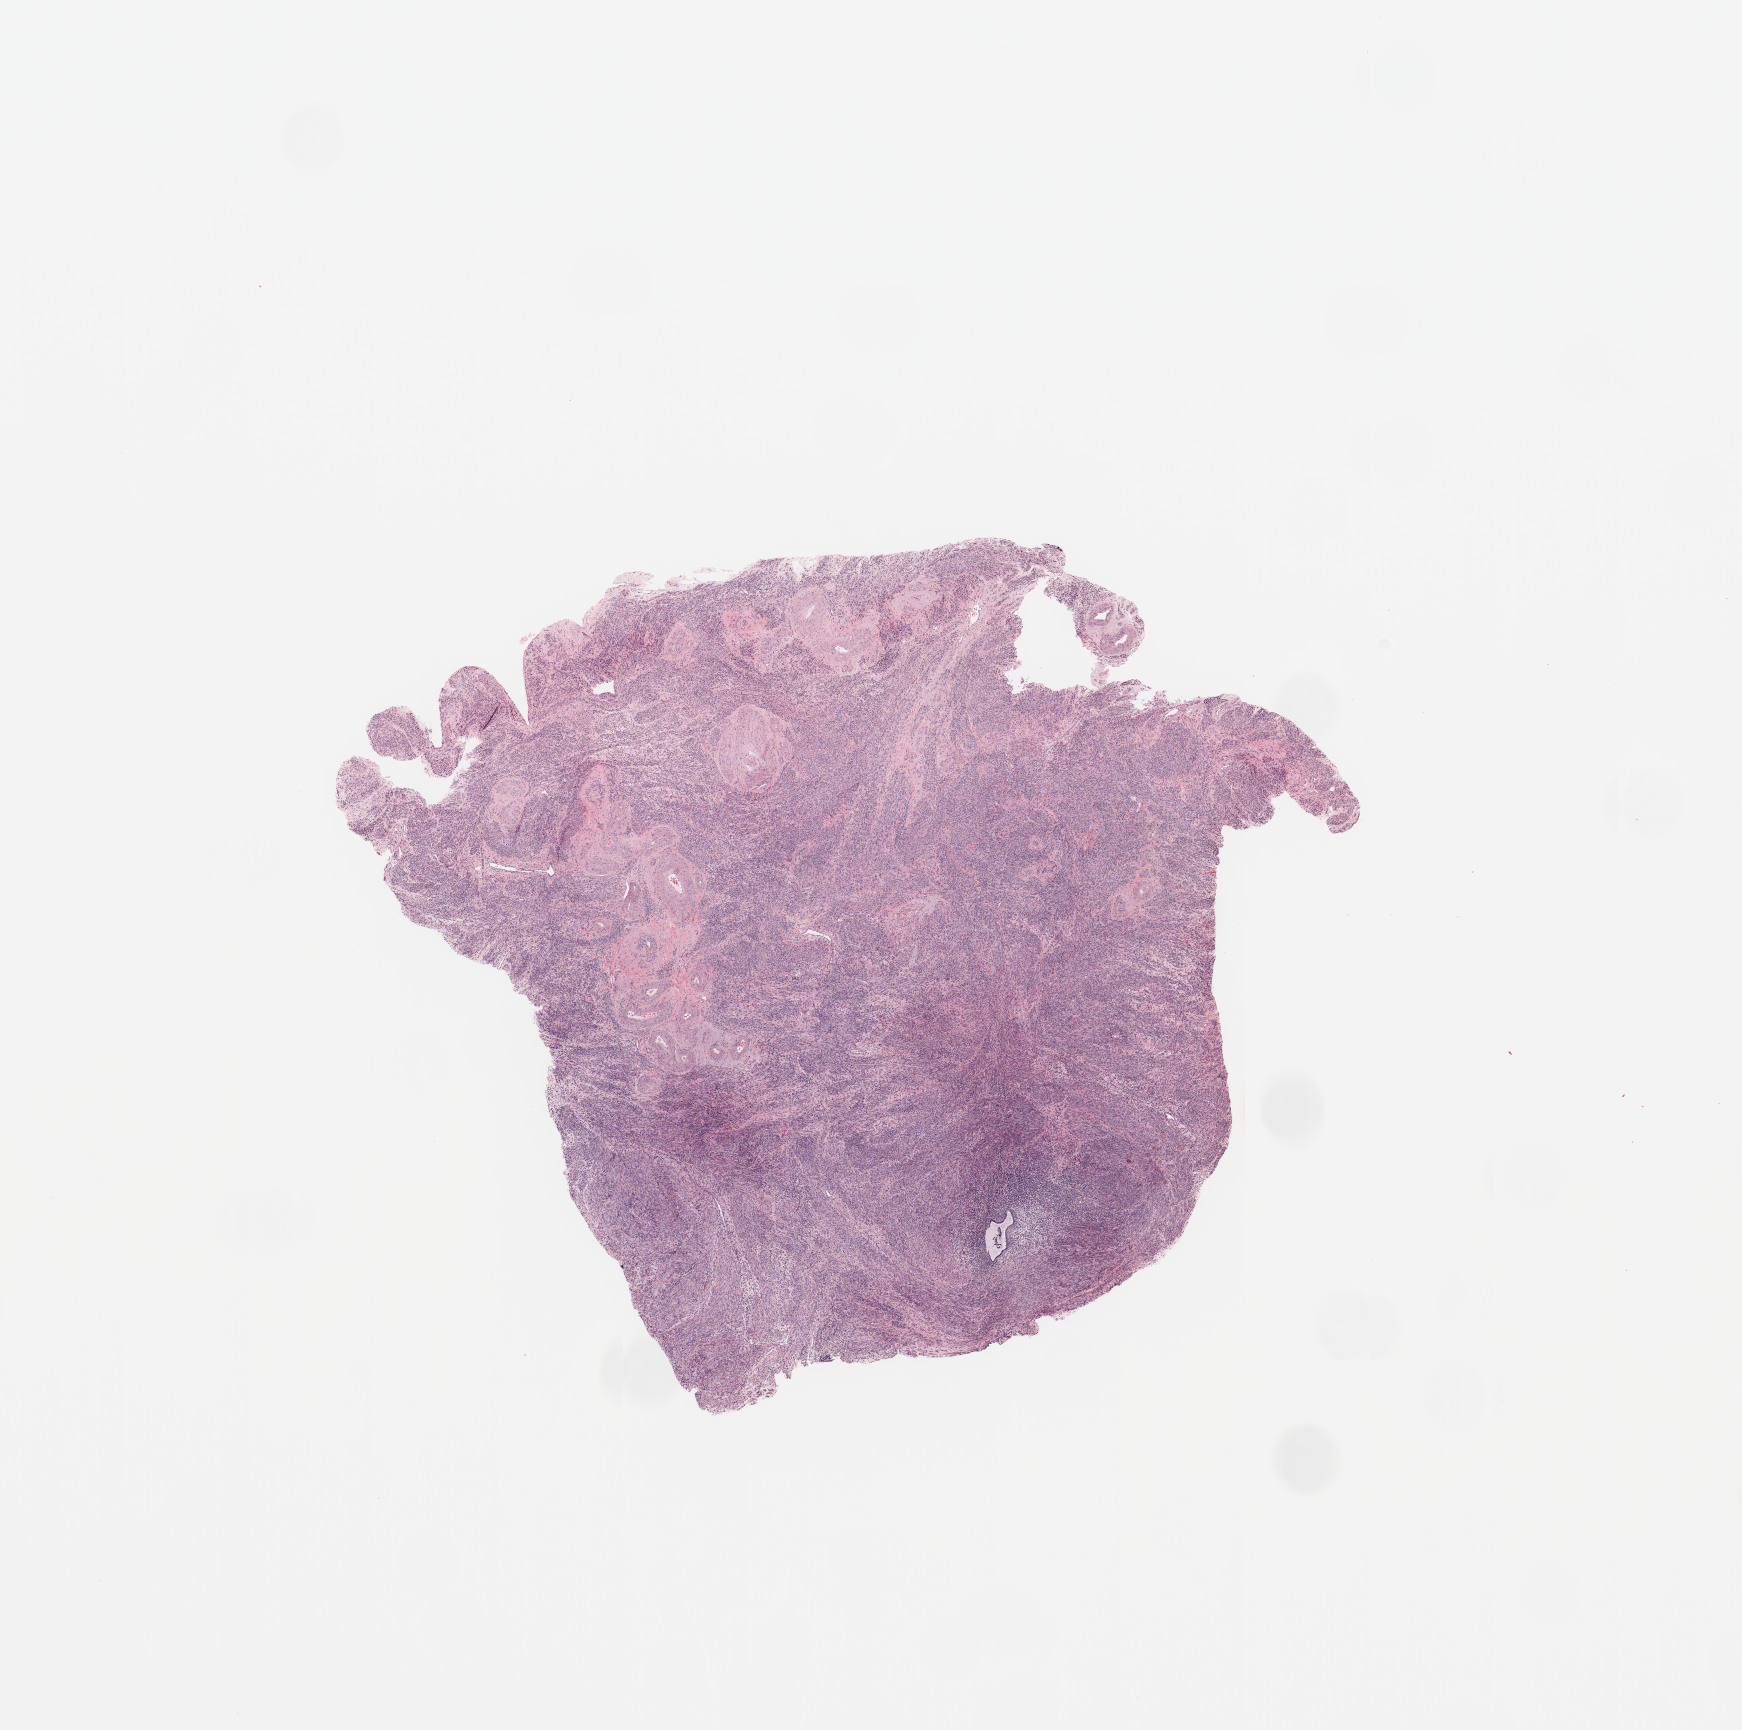
H&E whole-slide image — a low-resolution overview of the entire scanned area, about 13.8 x 13.7 mm (slide scanned at 20x), normal (non-tumour) tissue sample, uterus. 78-year-old female patient.
This section: normal (non-tumour) tissue from the same patient. Patient diagnosis: Endometrioid adenocarcinoma, NOS.